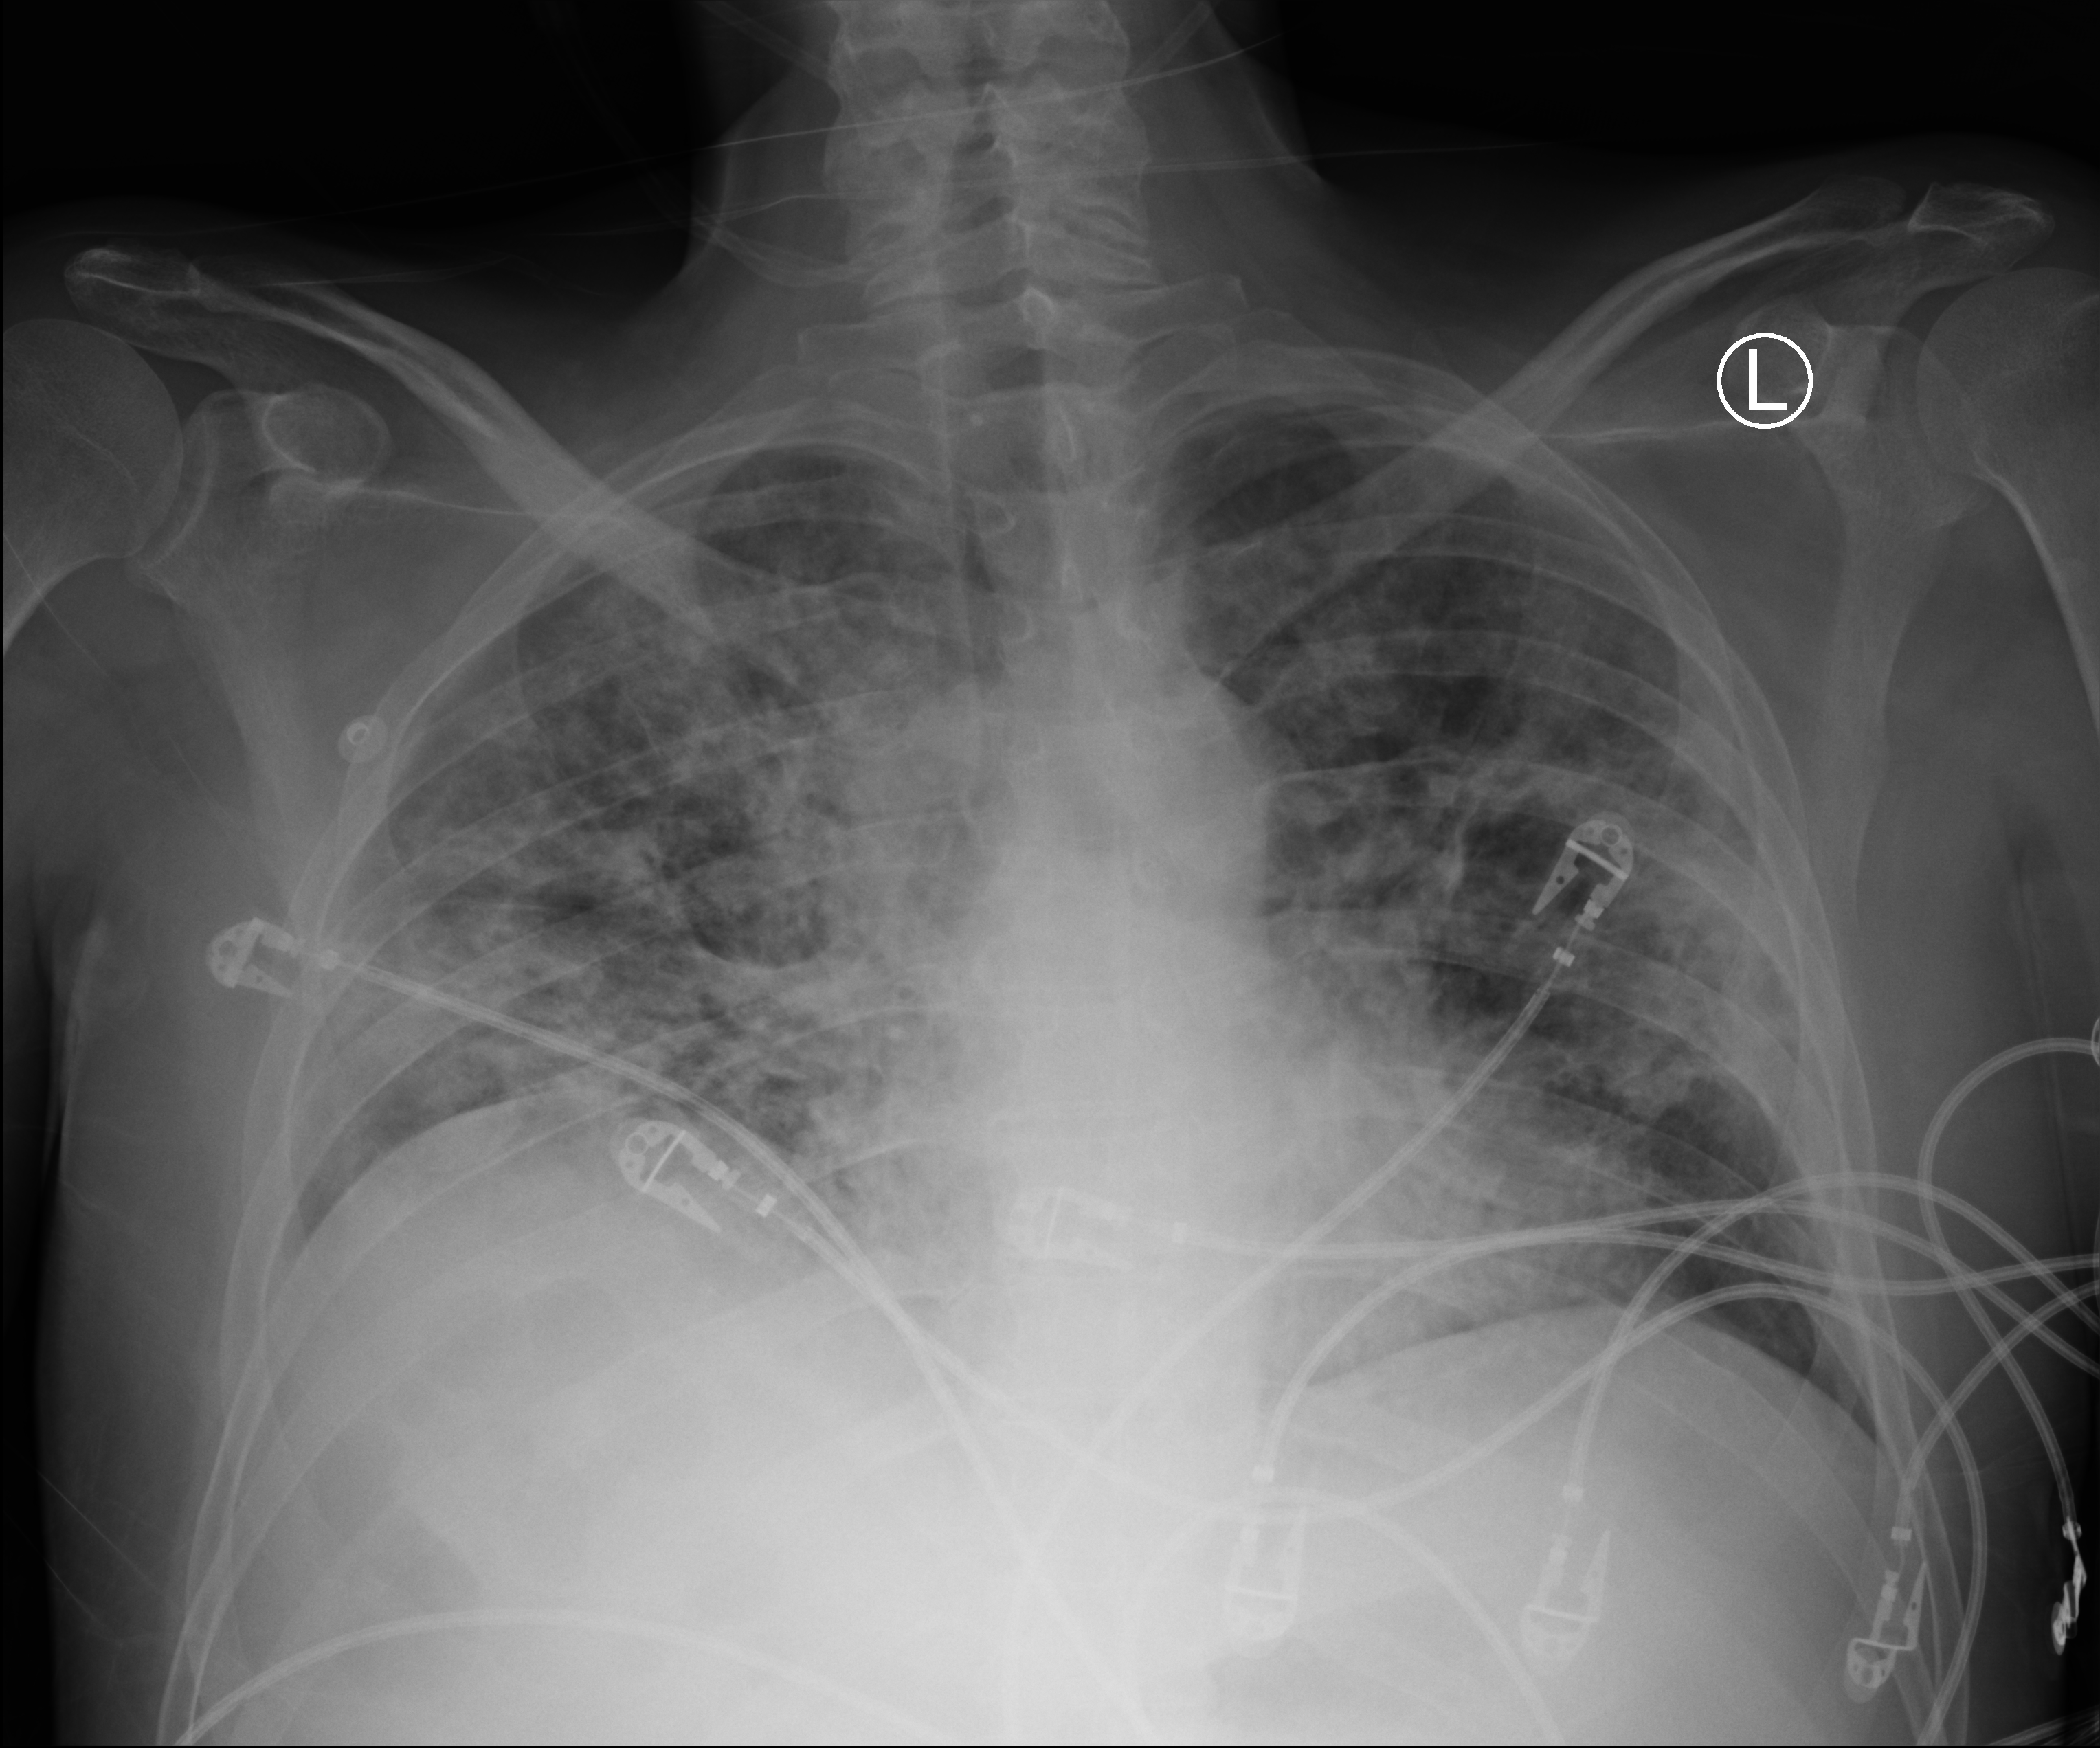
Chest X-ray (portable); anteroposterior (AP) projection. Patient hospitalised with COVID-19; male, aged 18–59 years.
Admission-level facts for this patient (not findings on this image; timing relative to this image not recorded):
- diabetes (admission record): no
- length of hospital stay: 48 days
- mechanically ventilated during this hospital stay: yes